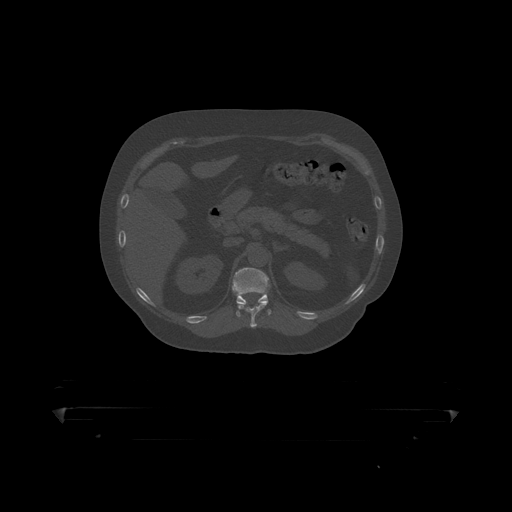
CT including the spine, one axial slice; slice 182 of 390 in the series (ordered by position); 120 kVp; bone window (W 1800 / L 400 HU); 1.25 mm slice thickness; 512 × 512 image matrix. Patient: male, 60 years. Case-level facts recorded for this patient, not image findings: primary cancer: prostate.
Outlined on this slice (semi-automatic segmentation, software-assisted and operator-edited):
- T11 vertebra: bounding box <238,303,268,319> (left, top, right, bottom; pixels)
- T12 vertebra: <232,267,272,317>